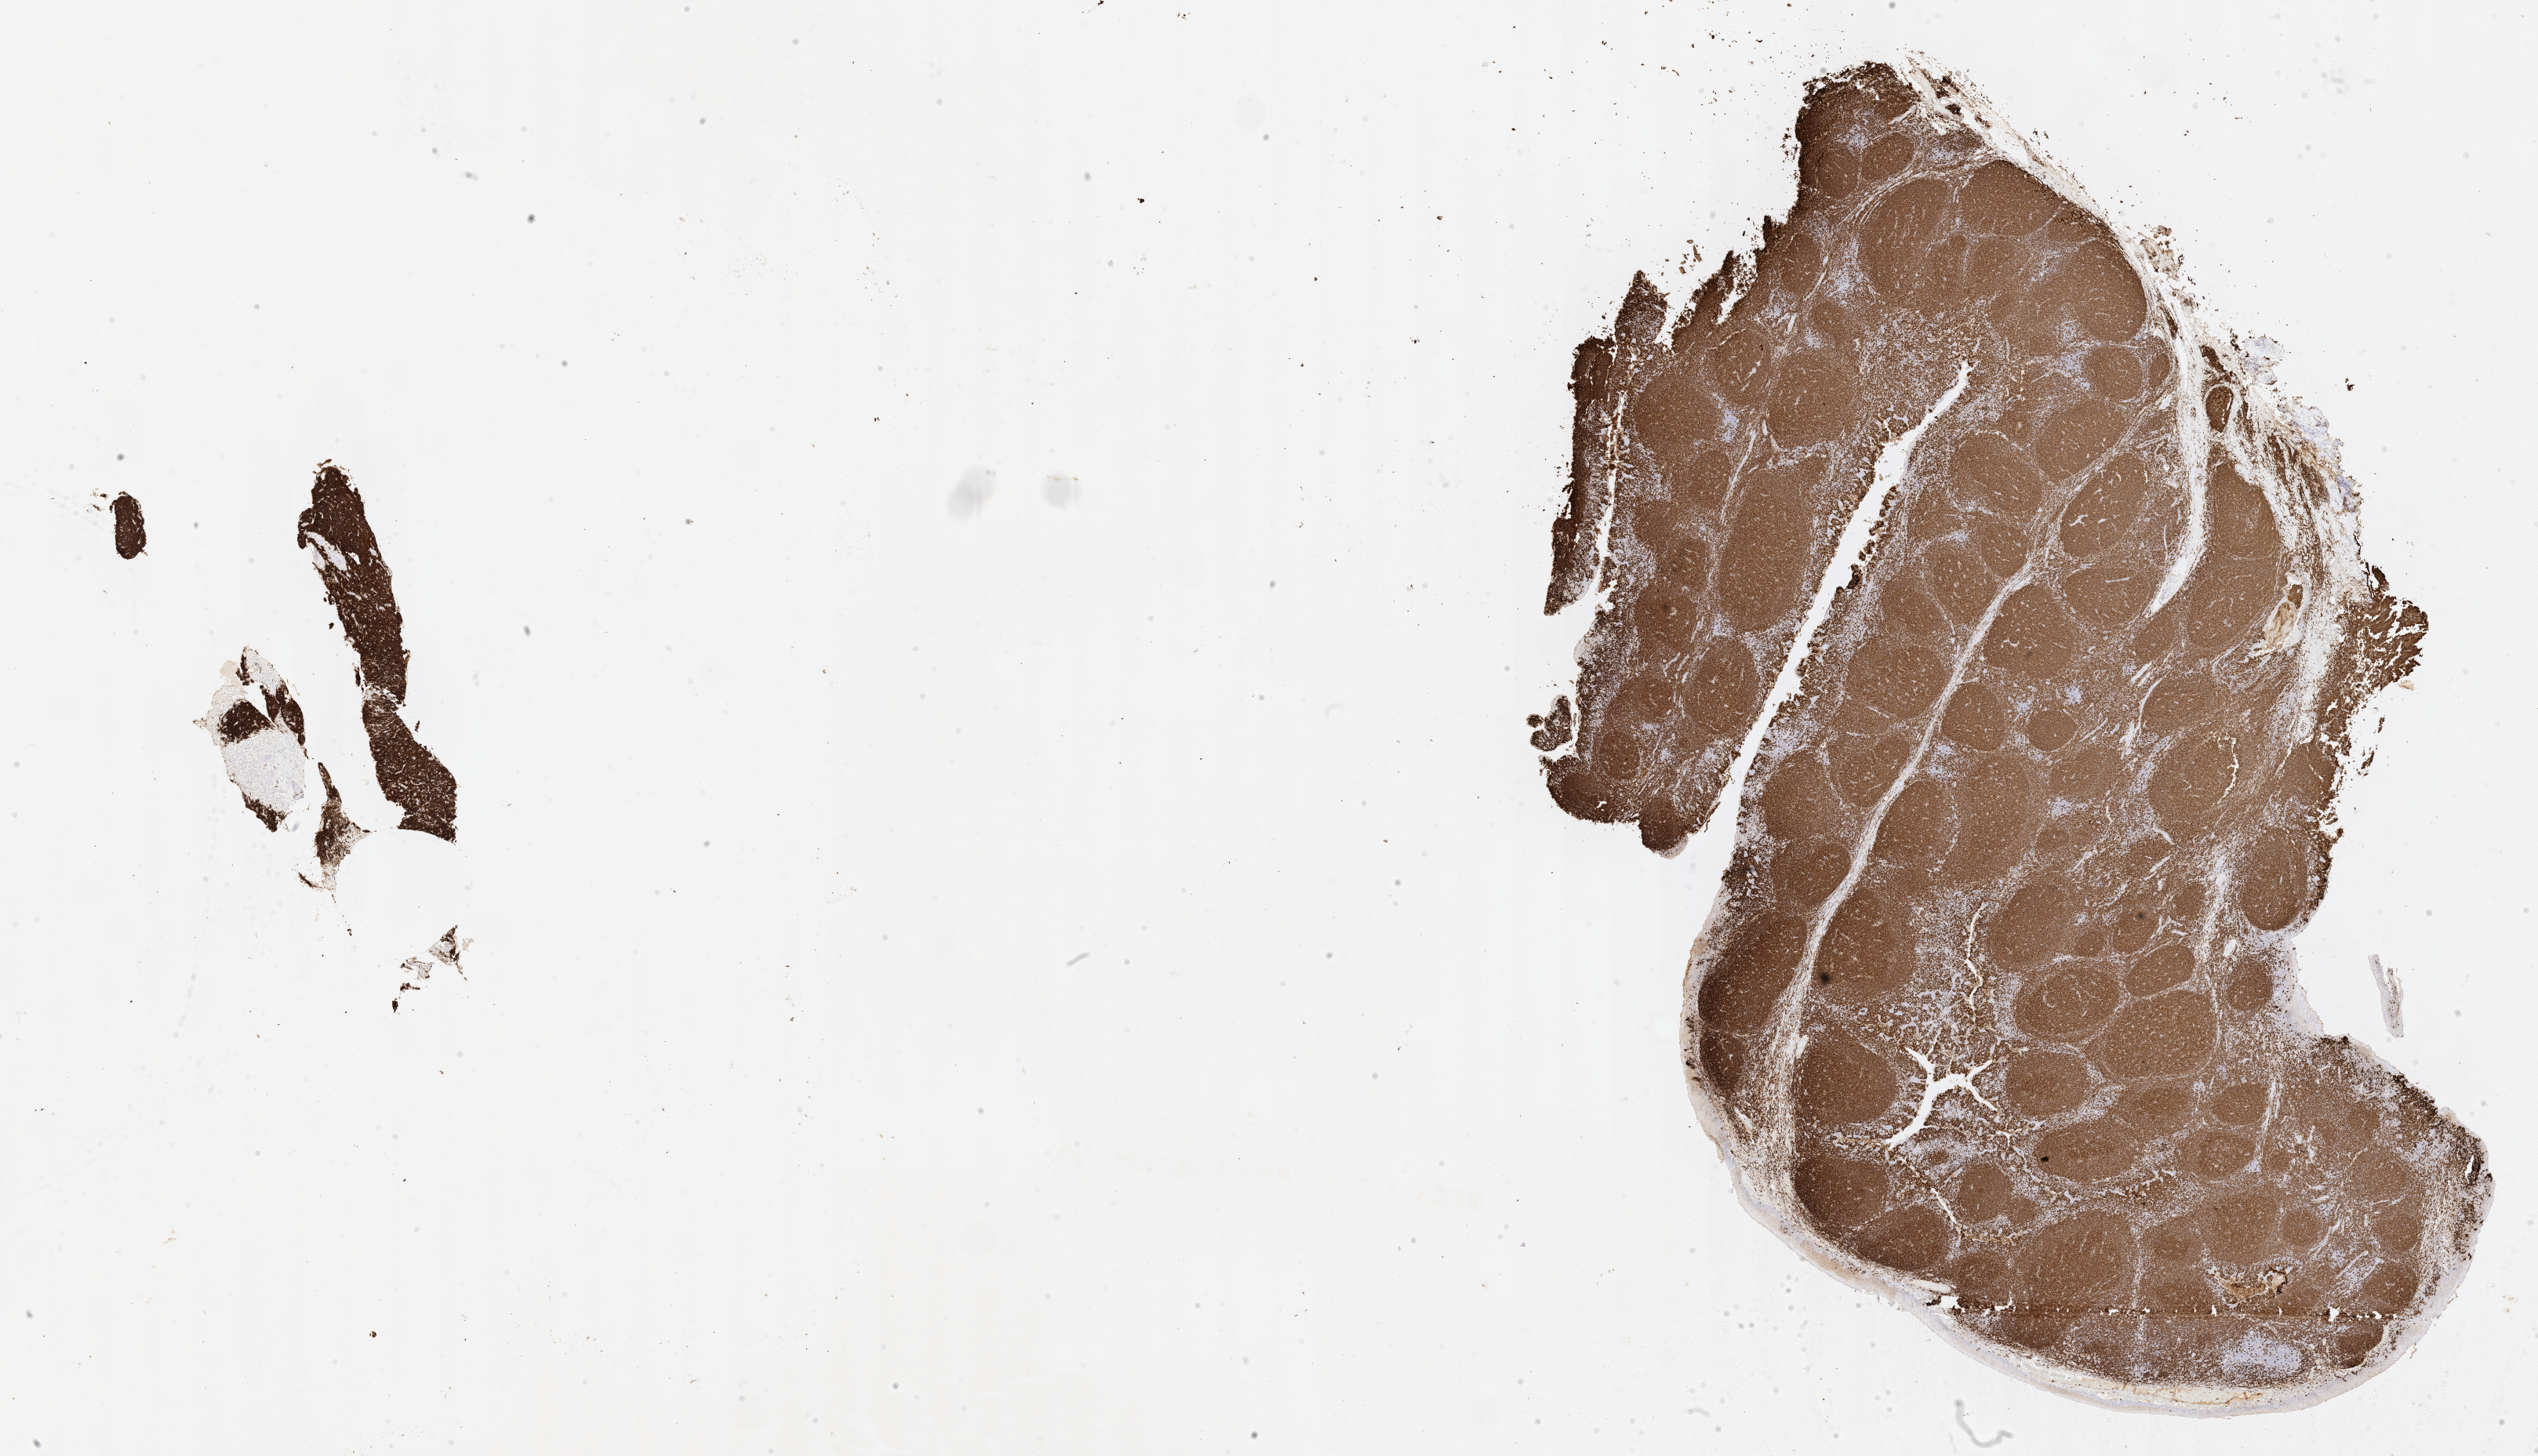
Whole-slide image, immunohistochemical stain for CD20 — whole scanned area (about 26.2 x 15.0 mm) shown as a low-resolution overview; tumor tissue; anatomic site: mandible. Patient: male, age at initial diagnosis 6 years.
* histologic diagnosis: Burkitt lymphoma, NOS